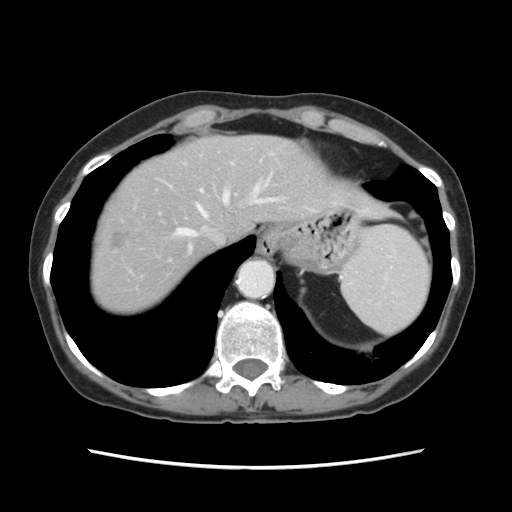
Contrast-enhanced abdominal CT, one axial slice. Slice 100 of 120 in the series (ordered by position). 120 kVp. Intravenous contrast given. Soft-tissue window (W 400 / L 40 HU). 2.5 mm slice thickness. 512 × 512 image matrix, field of view 330 × 330 mm. Female patient, age 70 years. From the clinical record (not read from this slice): diagnosis: colorectal cancer liver metastases, imaged before liver resection; multiple liver metastases: no; largest metastasis: 2.5 cm; chemotherapy before resection: yes.
Annotated regions visible in this slice (outlined manually by an expert reader):
- hepatic veins: bounding box <177,186,273,242> (left, top, right, bottom; pixels)
- liver: <92,137,349,312>
- planned liver remnant (the part of the liver to remain after resection): <147,136,351,261>
- portal vein (with intrahepatic branches): <200,190,203,193>
- liver metastasis: <112,233,129,247>